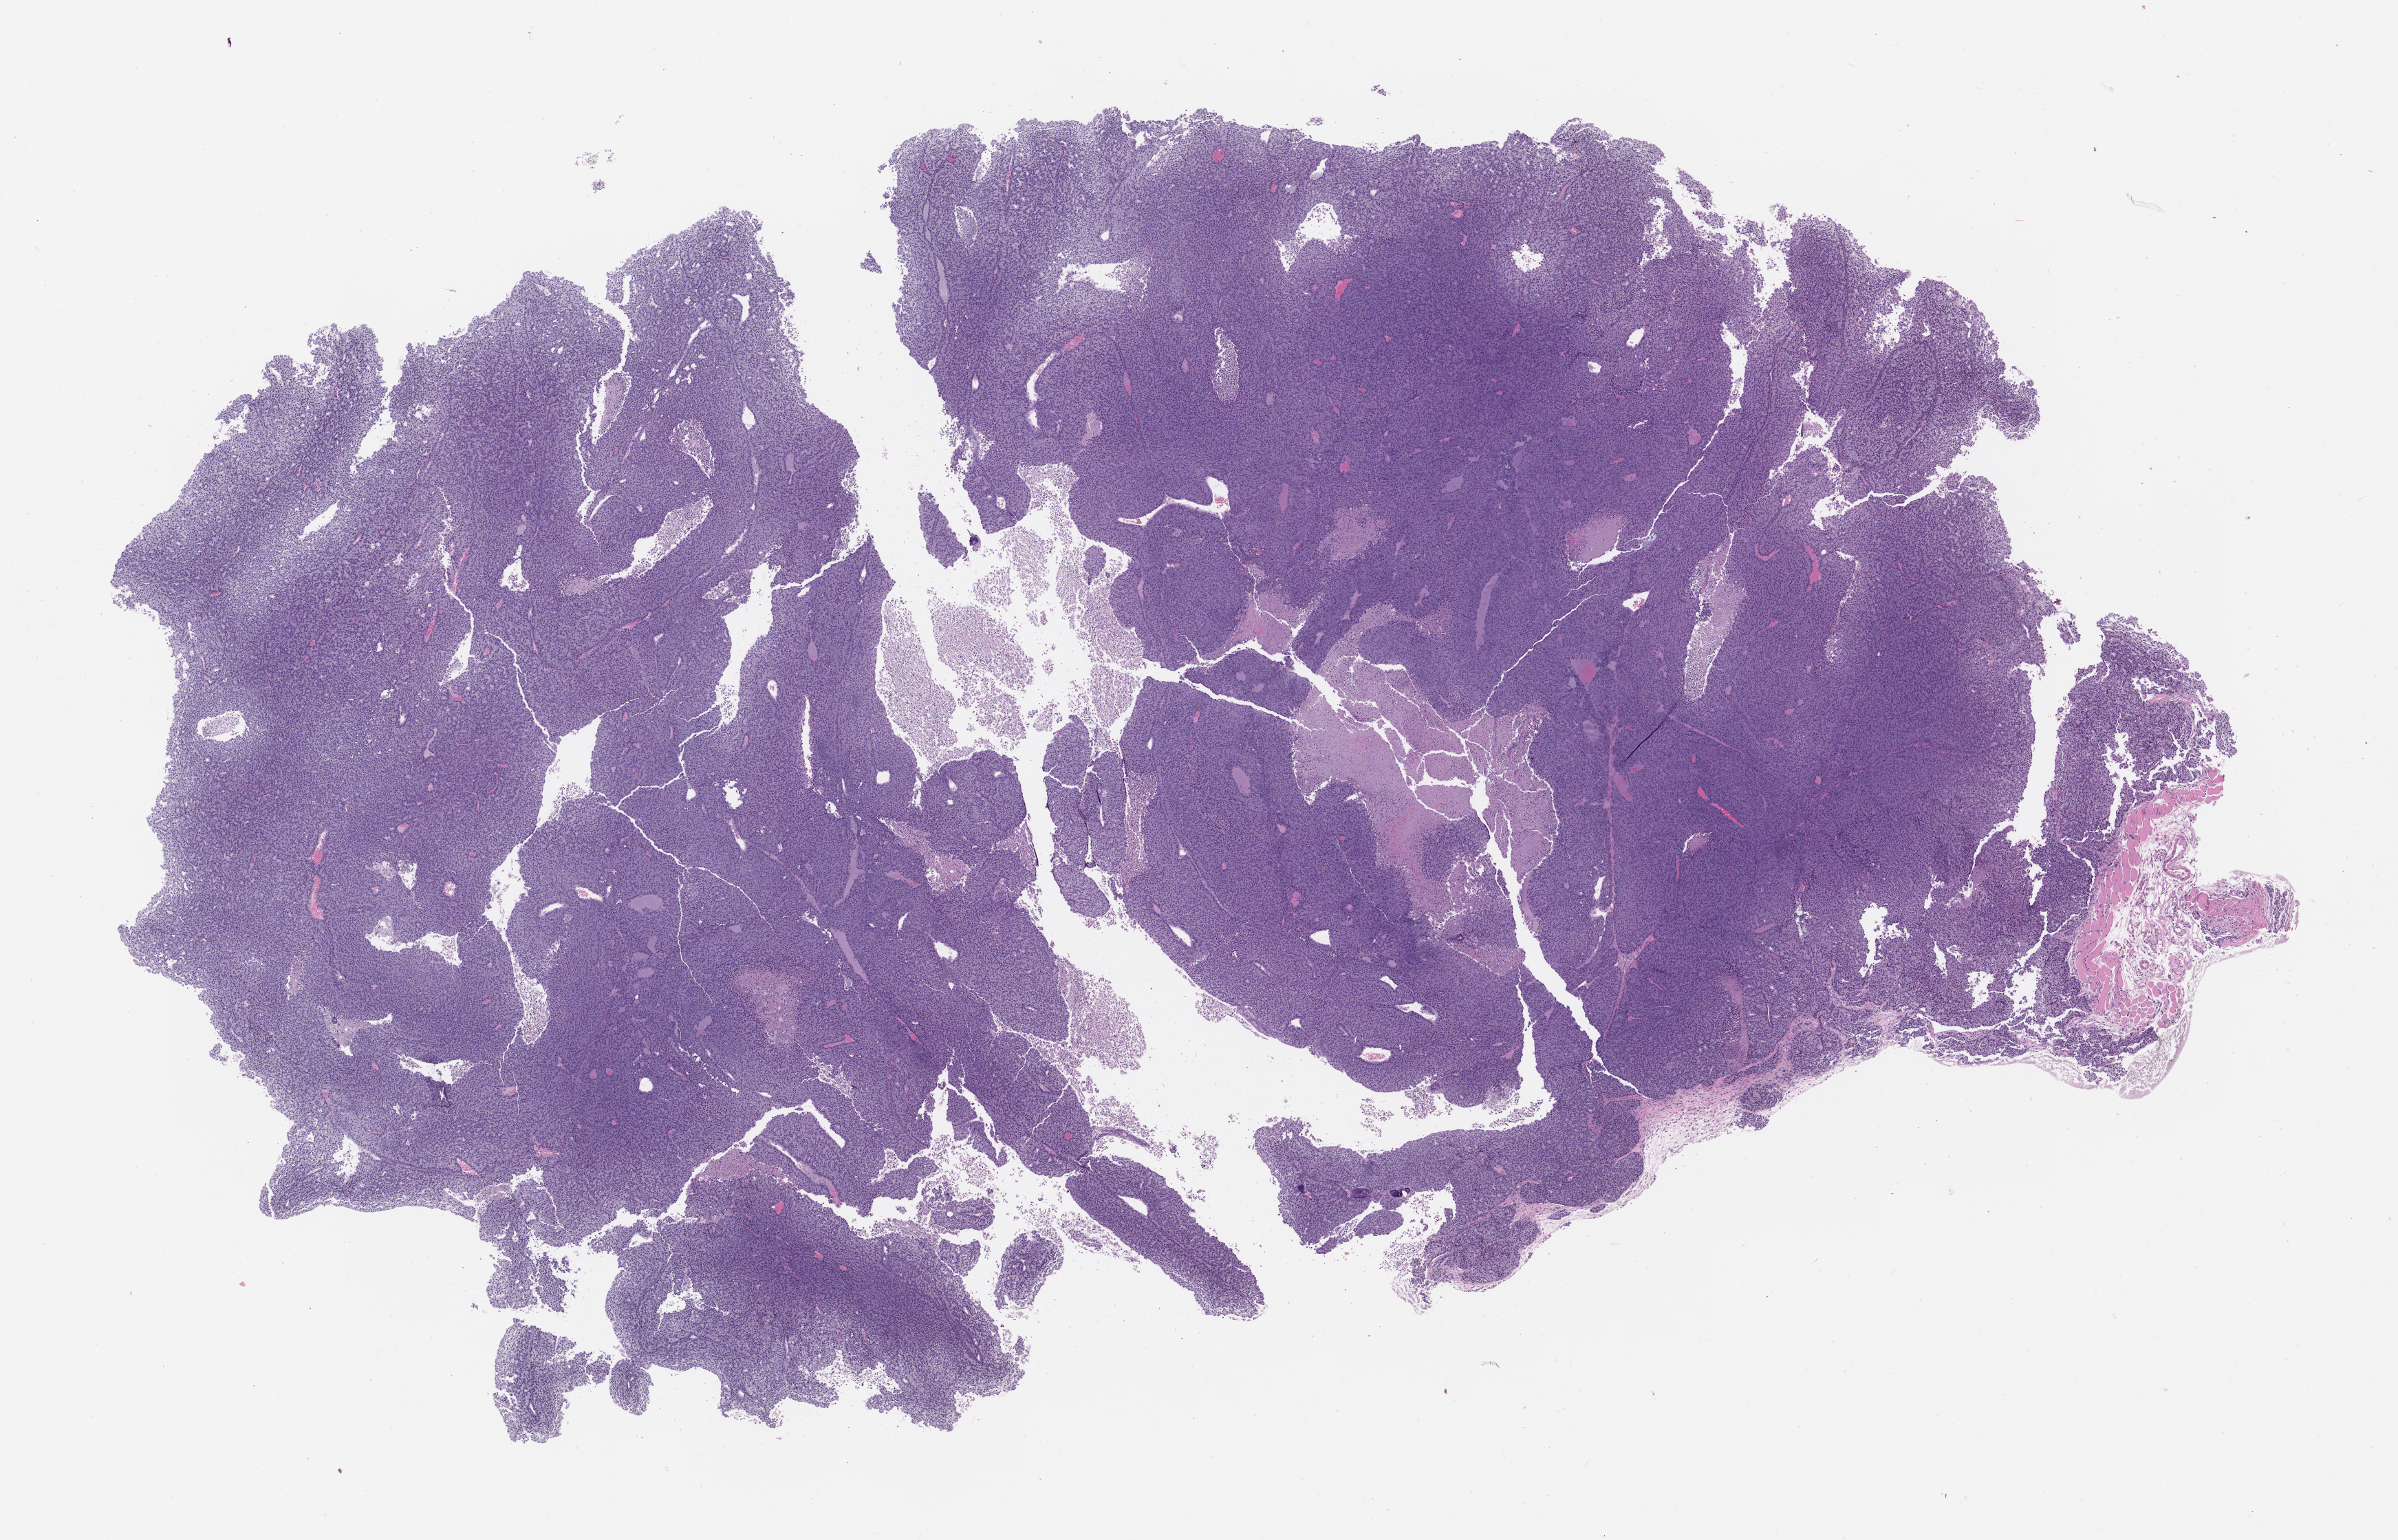
Whole-slide image, hematoxylin and eosin (H&E): patient-derived xenograft (human tumor grown in a mouse), passage 1, a low-resolution overview of the entire scanned area, about 14.0 x 9.0 mm; formalin-fixed, paraffin-embedded (FFPE) tissue; originating tumor site category: head and neck.
* originating patient diagnosis: Acinar Cell Carcinoma